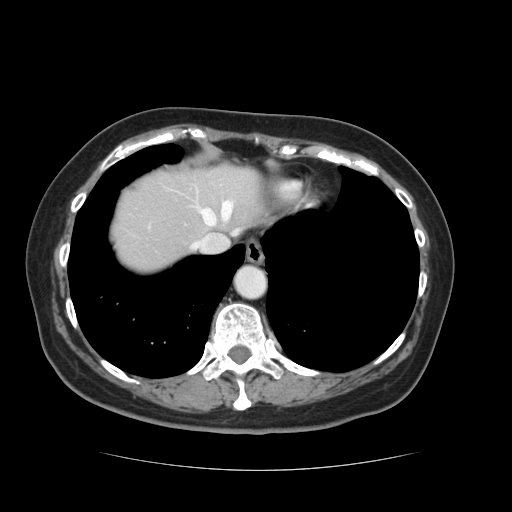
Contrast-enhanced abdominal CT, one axial slice; slice 111 of 128 in the series (ordered by position); 120 kVp; intravenous contrast given; soft-tissue window (W 400 / L 40 HU); 2.5 mm slice thickness; 512 × 512 image matrix, field of view 366 × 366 mm. Female patient, age 67 years. From the clinical record (not read from this slice): diagnosis: colorectal cancer liver metastases, imaged before liver resection; multiple liver metastases: yes; largest metastasis: 3 cm; disease in both lobes: yes.
Outlined on this slice (expert manual segmentation):
- hepatic veins: bounding box <191,200,234,251> (left, top, right, bottom; pixels)
- liver: <111,163,262,272>
- planned liver remnant (the part of the liver to remain after resection): <111,165,262,272>